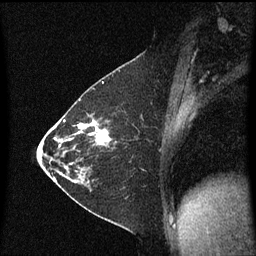
Breast MRI (dynamic contrast-enhanced), one sagittal slice; slice 30 of 60 in the series (ordered by position); dynamic contrast-enhanced series, image 2 of 3 at this slice position (ordered by acquisition); 1.5 T; TE 4.2 ms, TR 8.4 ms; 2 mm slice thickness; 256 × 256 image matrix. Patient: female, 36 years. Case-level facts recorded for this patient, not image findings: setting: breast cancer imaged before/during neoadjuvant chemotherapy; receptor status: HR-positive, HER2-negative.
Structures marked on this image (semi-automatic segmentation, software-assisted and operator-edited):
- analysis volume of interest (the breast-tissue region the enhancement analysis was run in; not a lesion): box from (x=72, y=116) to (x=117, y=187) px
- tumour enhancement mask (voxels above the 70 % enhancement threshold inside the analysis volume of interest): (x=76, y=120)–(x=111, y=183)